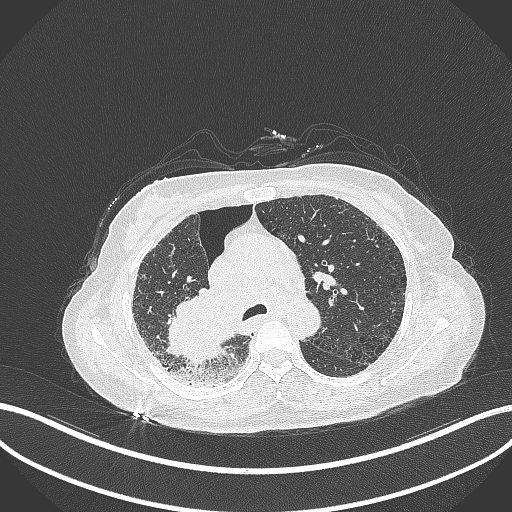
Chest CT, one axial slice; slice 229 of 408 in the series (ordered by position); reconstruction kernel B70f; lung window (W 1500 / L -600 HU); 512 × 512 image matrix, field of view 400 × 400 mm. Female patient, age 64 years. Case-level facts recorded for this patient, not image findings: clinical TNM (as recorded): T3 N3 M0.
Annotated regions visible in this slice (bounding box drawn by a radiologist):
- lung tumour (recorded histology: squamous cell carcinoma): bounding box [x1, y1, x2, y2] px = [162, 284, 237, 371]